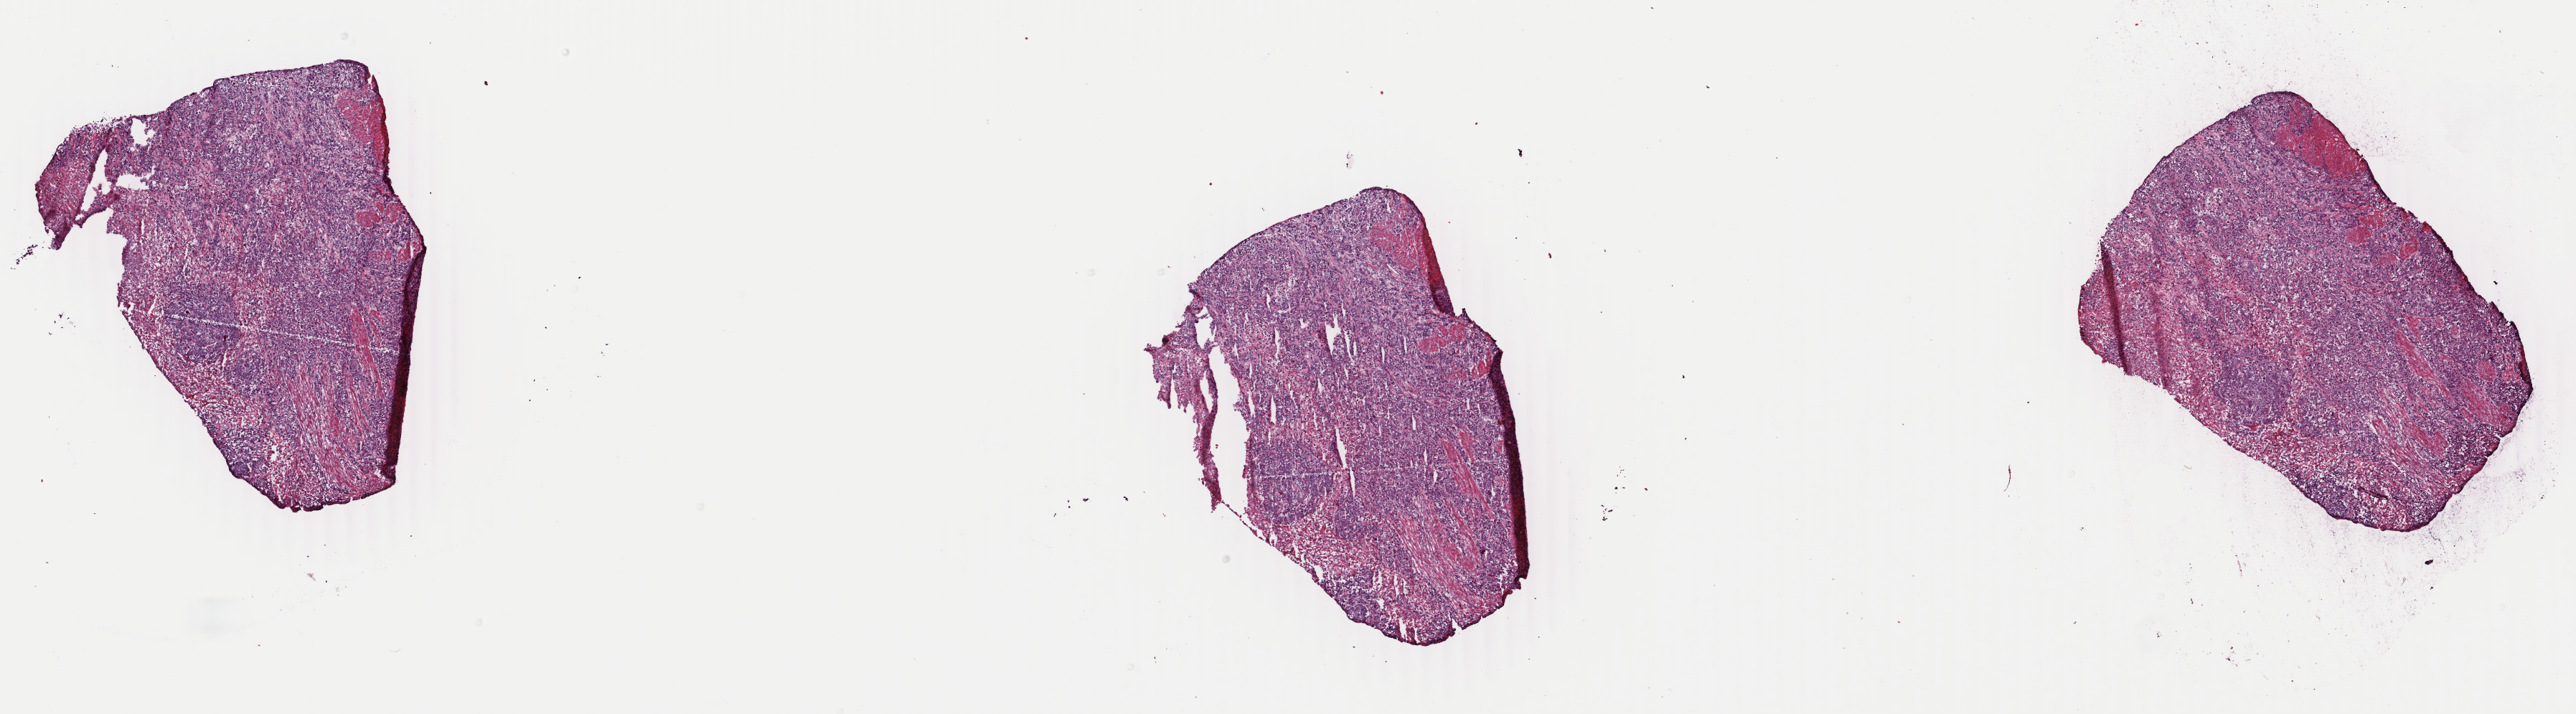
Digitized H&E tissue section (whole slide) — low-resolution overview of the scanned area, about 28.6 x 7.9 mm (acquisition: 40x scan); frozen section; sample: primary tumour, bladder. Male, age 60 years at initial diagnosis. Histologic grade: high grade. Slide review estimates, as recorded: tumour cells 72%, tumour nuclei 85%, normal cells 8%, stromal cells 0%, necrosis 20%. Infiltration values recorded for this section: lymphocyte infiltration 10%, monocyte infiltration 0%, neutrophil infiltration 1%.
• AJCC pathologic stage: II (5th edition)
• pathologic diagnosis: Transitional cell carcinoma